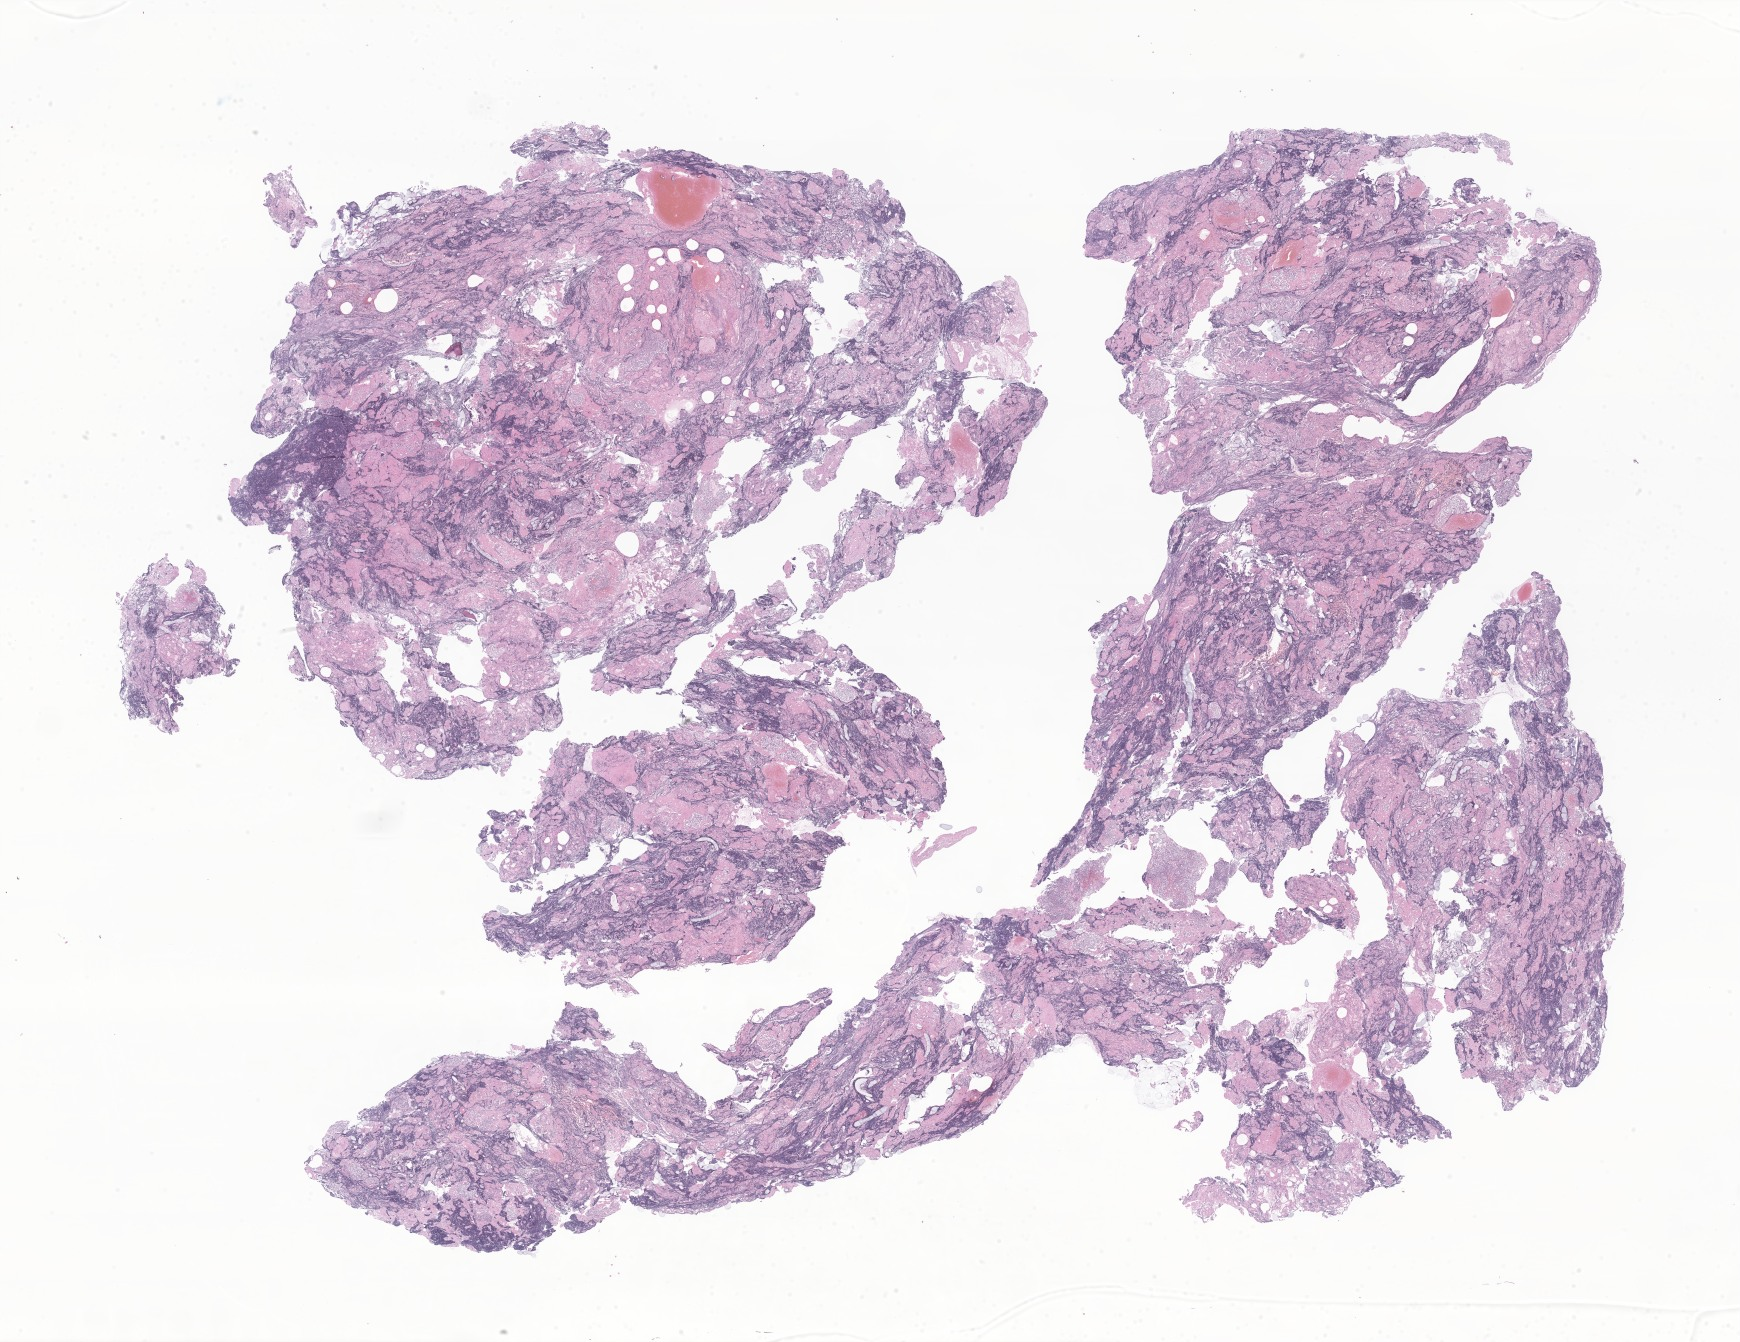
Whole-slide image, H&E stain of tumor tissue from the brain — a low-resolution overview of the entire scanned area, about 29.3 x 22.6 mm, formalin-fixed paraffin-embedded section. Patient female; age 110 months (9 years 2 months).
- recorded diagnosis: Medulloblastoma, NOS